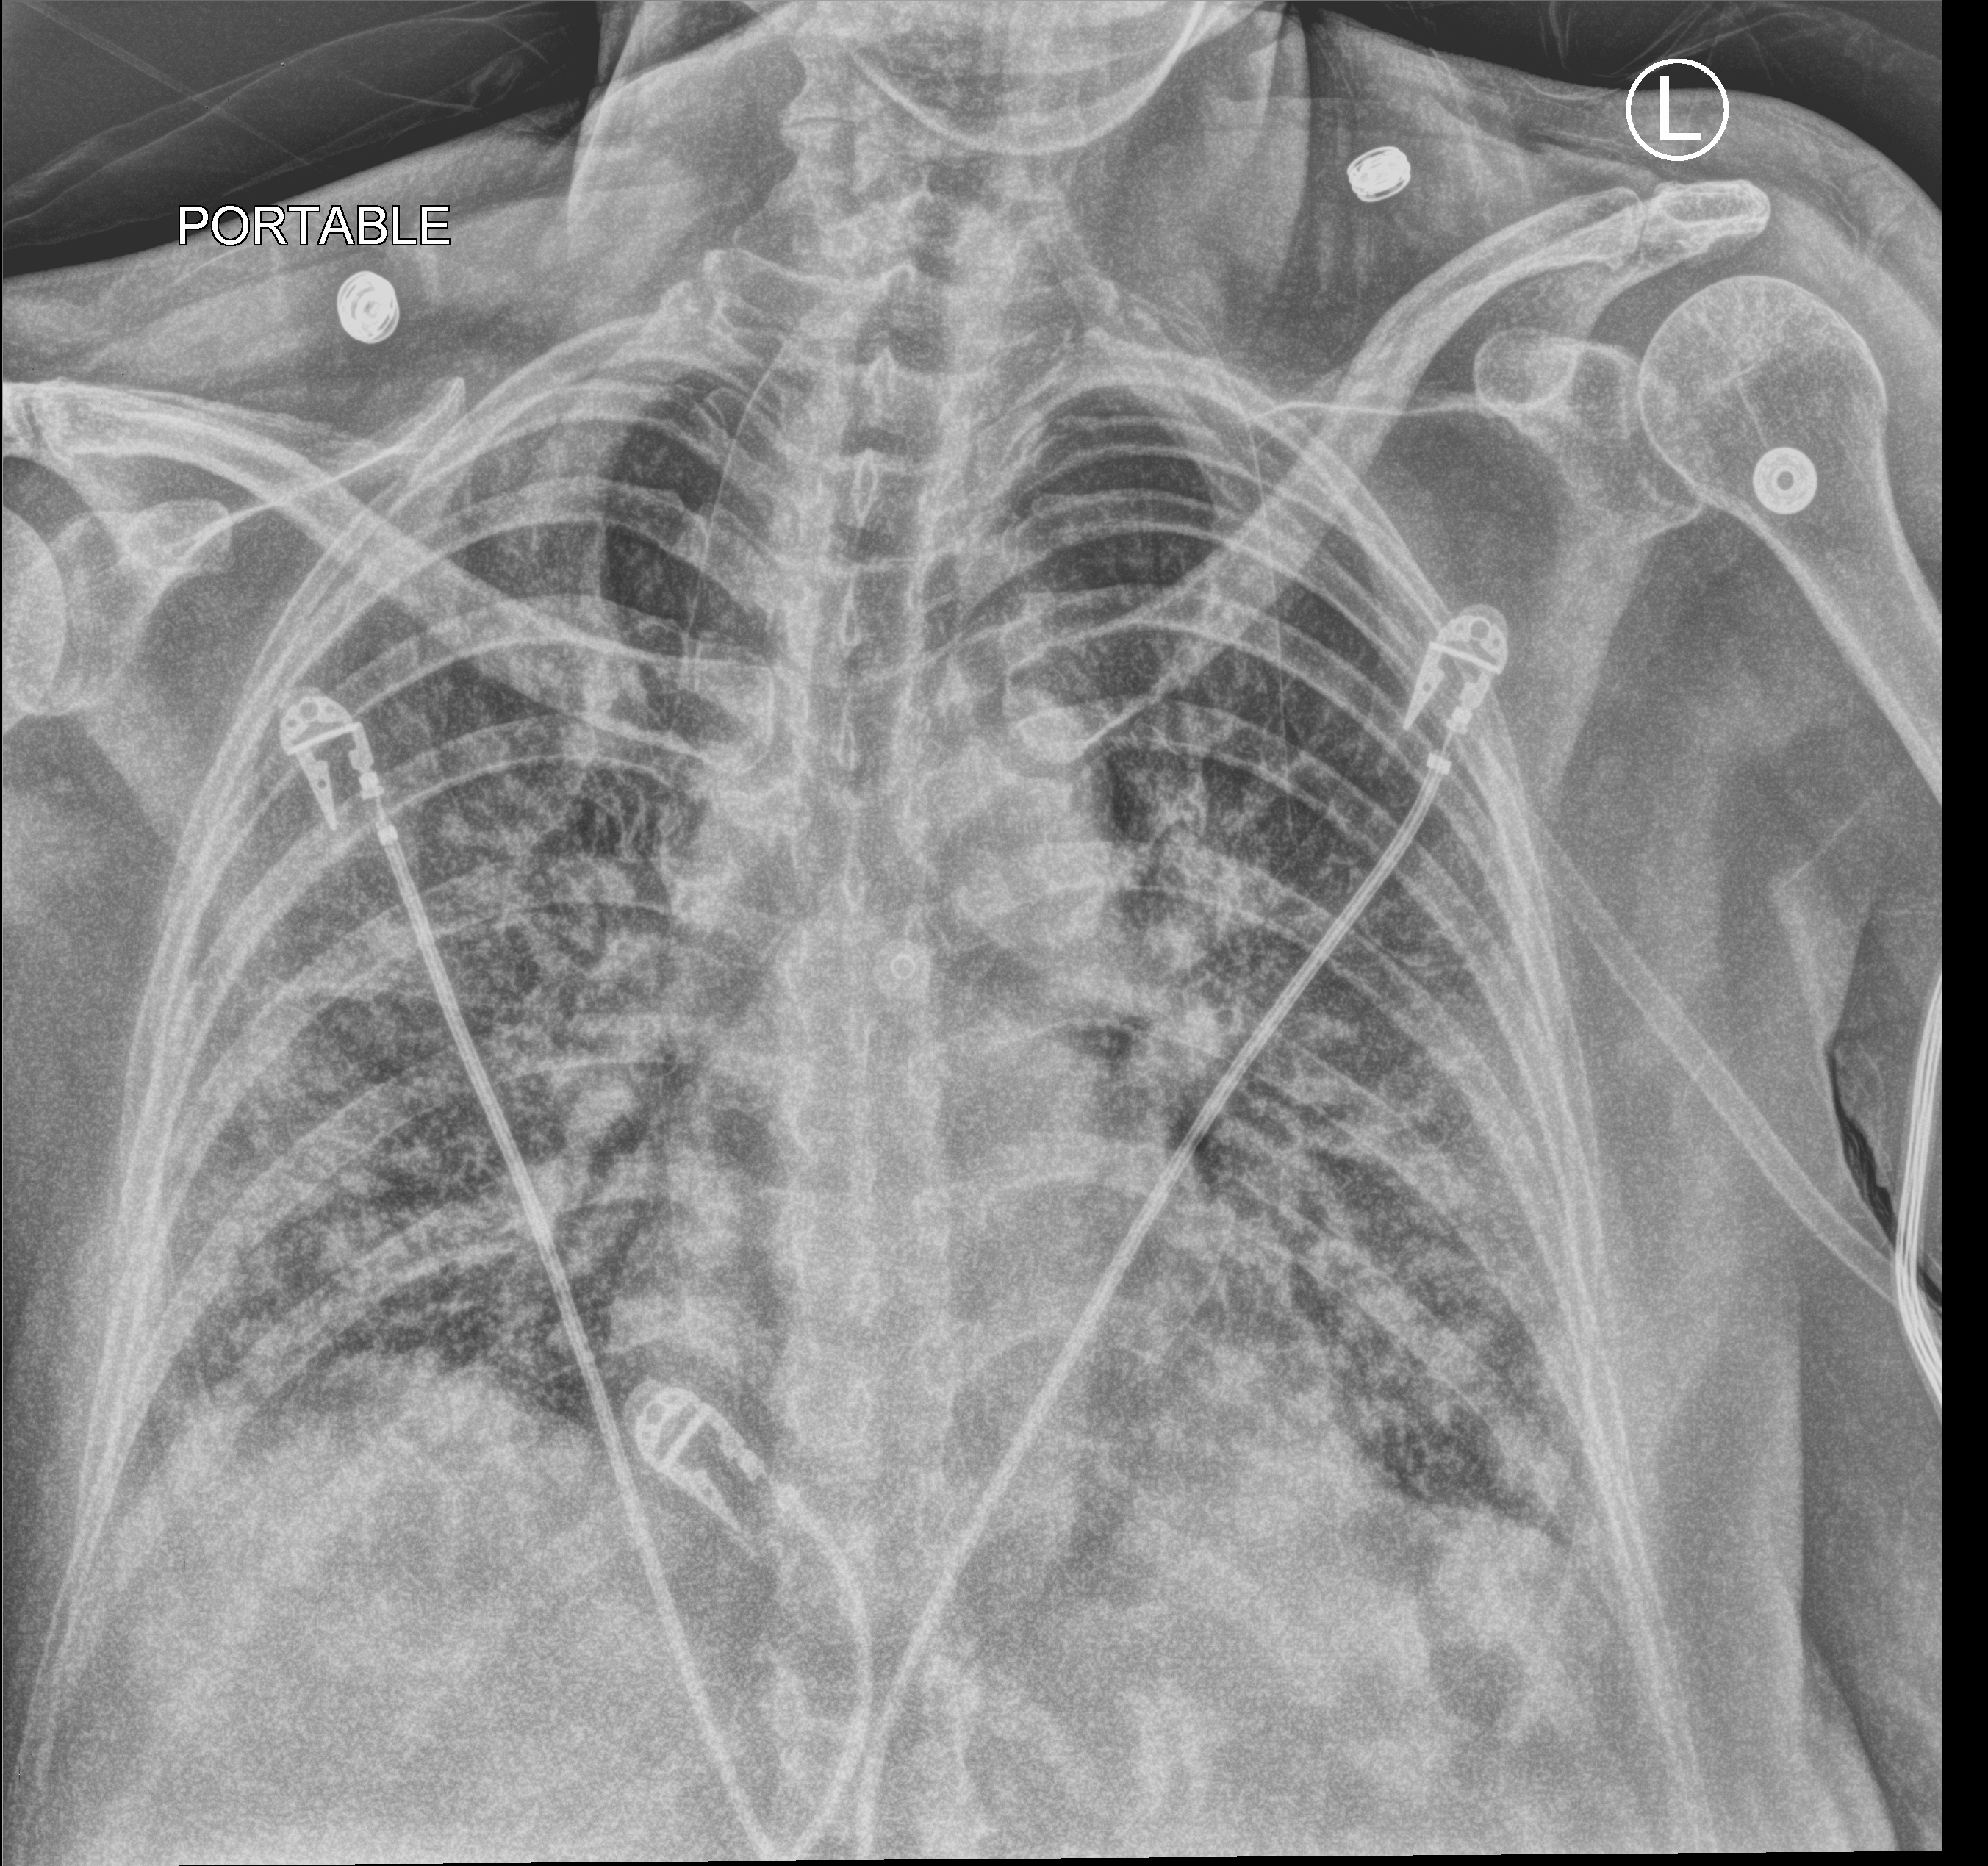
Portable chest radiograph; anteroposterior (AP) projection. Female patient hospitalised with COVID-19, age 60–74 years.
Admission-level facts for this patient (not findings on this image; timing relative to this image not recorded): admitted to intensive care during this hospital stay: yes; chronic kidney disease (admission record): no; mechanically ventilated during this hospital stay: yes.